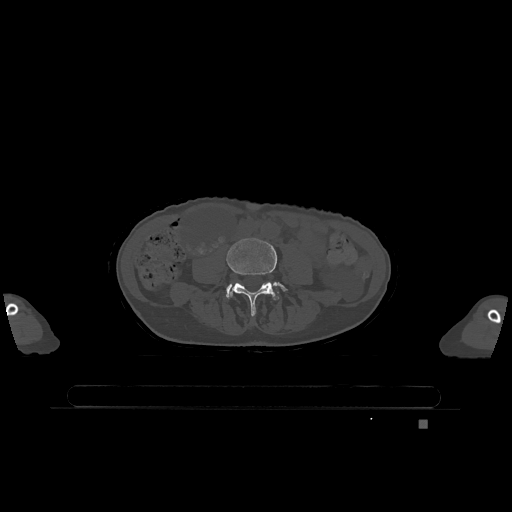
CT including the spine, one axial slice. Position 292 of 1317 along the scan axis. Bone window (W 1800 / L 400 HU). 512 × 512 image matrix, field of view 500 × 500 mm. Patient: female, 74 years. From the clinical record (not read from this slice): primary cancer: lung; vertebrae with lytic lesions (as recorded): T1, T4, T5, T6, L4, L5.
Annotated regions visible in this slice (semi-automatically segmented with operator editing):
- L4 vertebra: bounding box (x1, y1, x2, y2) in pixels: (226, 238, 288, 316)
- L5 vertebra: (226, 286, 279, 299)